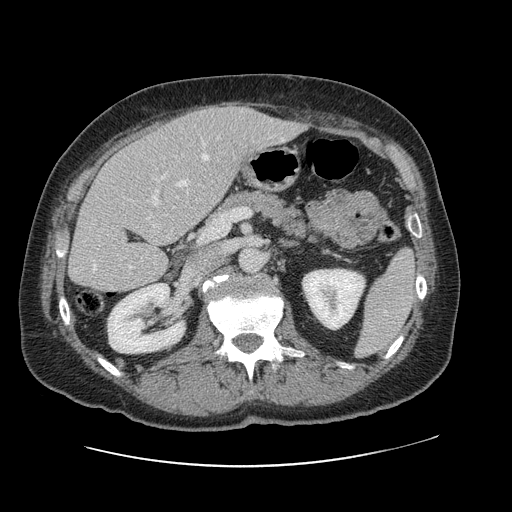
Contrast-enhanced abdominal CT, one axial slice; slice 52 of 138 in the series (ordered by position); 120 kVp; intravenous contrast given; soft-tissue window (W 400 / L 40 HU); 2.5 mm slice thickness; 512 × 512 image matrix, field of view 402 × 402 mm. Male patient, age 71 years. Case-level facts recorded for this patient, not image findings: diagnosis: colorectal cancer liver metastases, imaged before liver resection; multiple liver metastases: no; largest metastasis: 3.3 cm.
Annotated regions visible in this slice (manually delineated by an expert):
- hepatic veins: bounding box (x1, y1, x2, y2) in pixels: (93, 154, 227, 272)
- liver: (70, 103, 300, 293)
- planned liver remnant (the part of the liver to remain after resection): (70, 142, 198, 293)
- portal vein (with intrahepatic branches): (152, 174, 166, 206)